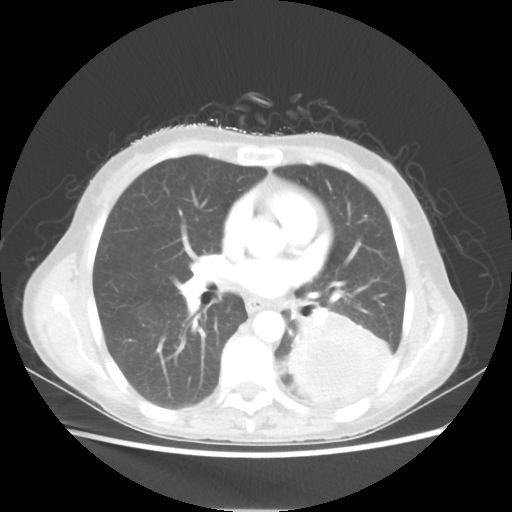
Chest CT, one axial slice; position 29 of 56 along the scan axis; lung window (W 1500 / L -600 HU); 512 × 512 image matrix, field of view 360 × 360 mm. Patient: female, 53 years. Case-level facts recorded for this patient, not image findings: clinical TNM (as recorded): T3 N0 M0.
Annotated regions visible in this slice (rectangle marked by the reading radiologist):
- lung tumour (recorded histology: adenocarcinoma): bounding box (x1, y1, x2, y2) in pixels: (287, 310, 391, 403)